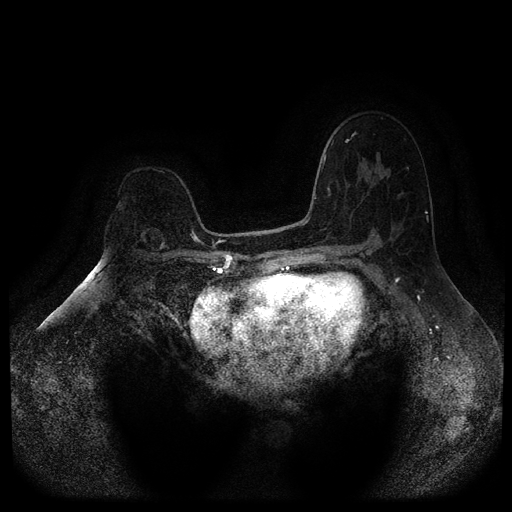
Breast MRI (dynamic contrast-enhanced, multi-phase), one axial slice; position 69 of 116 along the scan axis; dynamic contrast-enhanced series, time point 2 of 5 at this slice position (early post-contrast); 1.5 T; TE 2.6 ms, TR 5.4 ms; 2 mm slice thickness; 512 × 512 image matrix, field of view 340 × 340 mm. Patient: female, 64 years.
Annotated regions visible in this slice (semi-automatic segmentation, software-assisted and operator-edited):
- breast lesion (labelled benign in the annotation): bounding box [x1, y1, x2, y2] px = [138, 228, 170, 250]